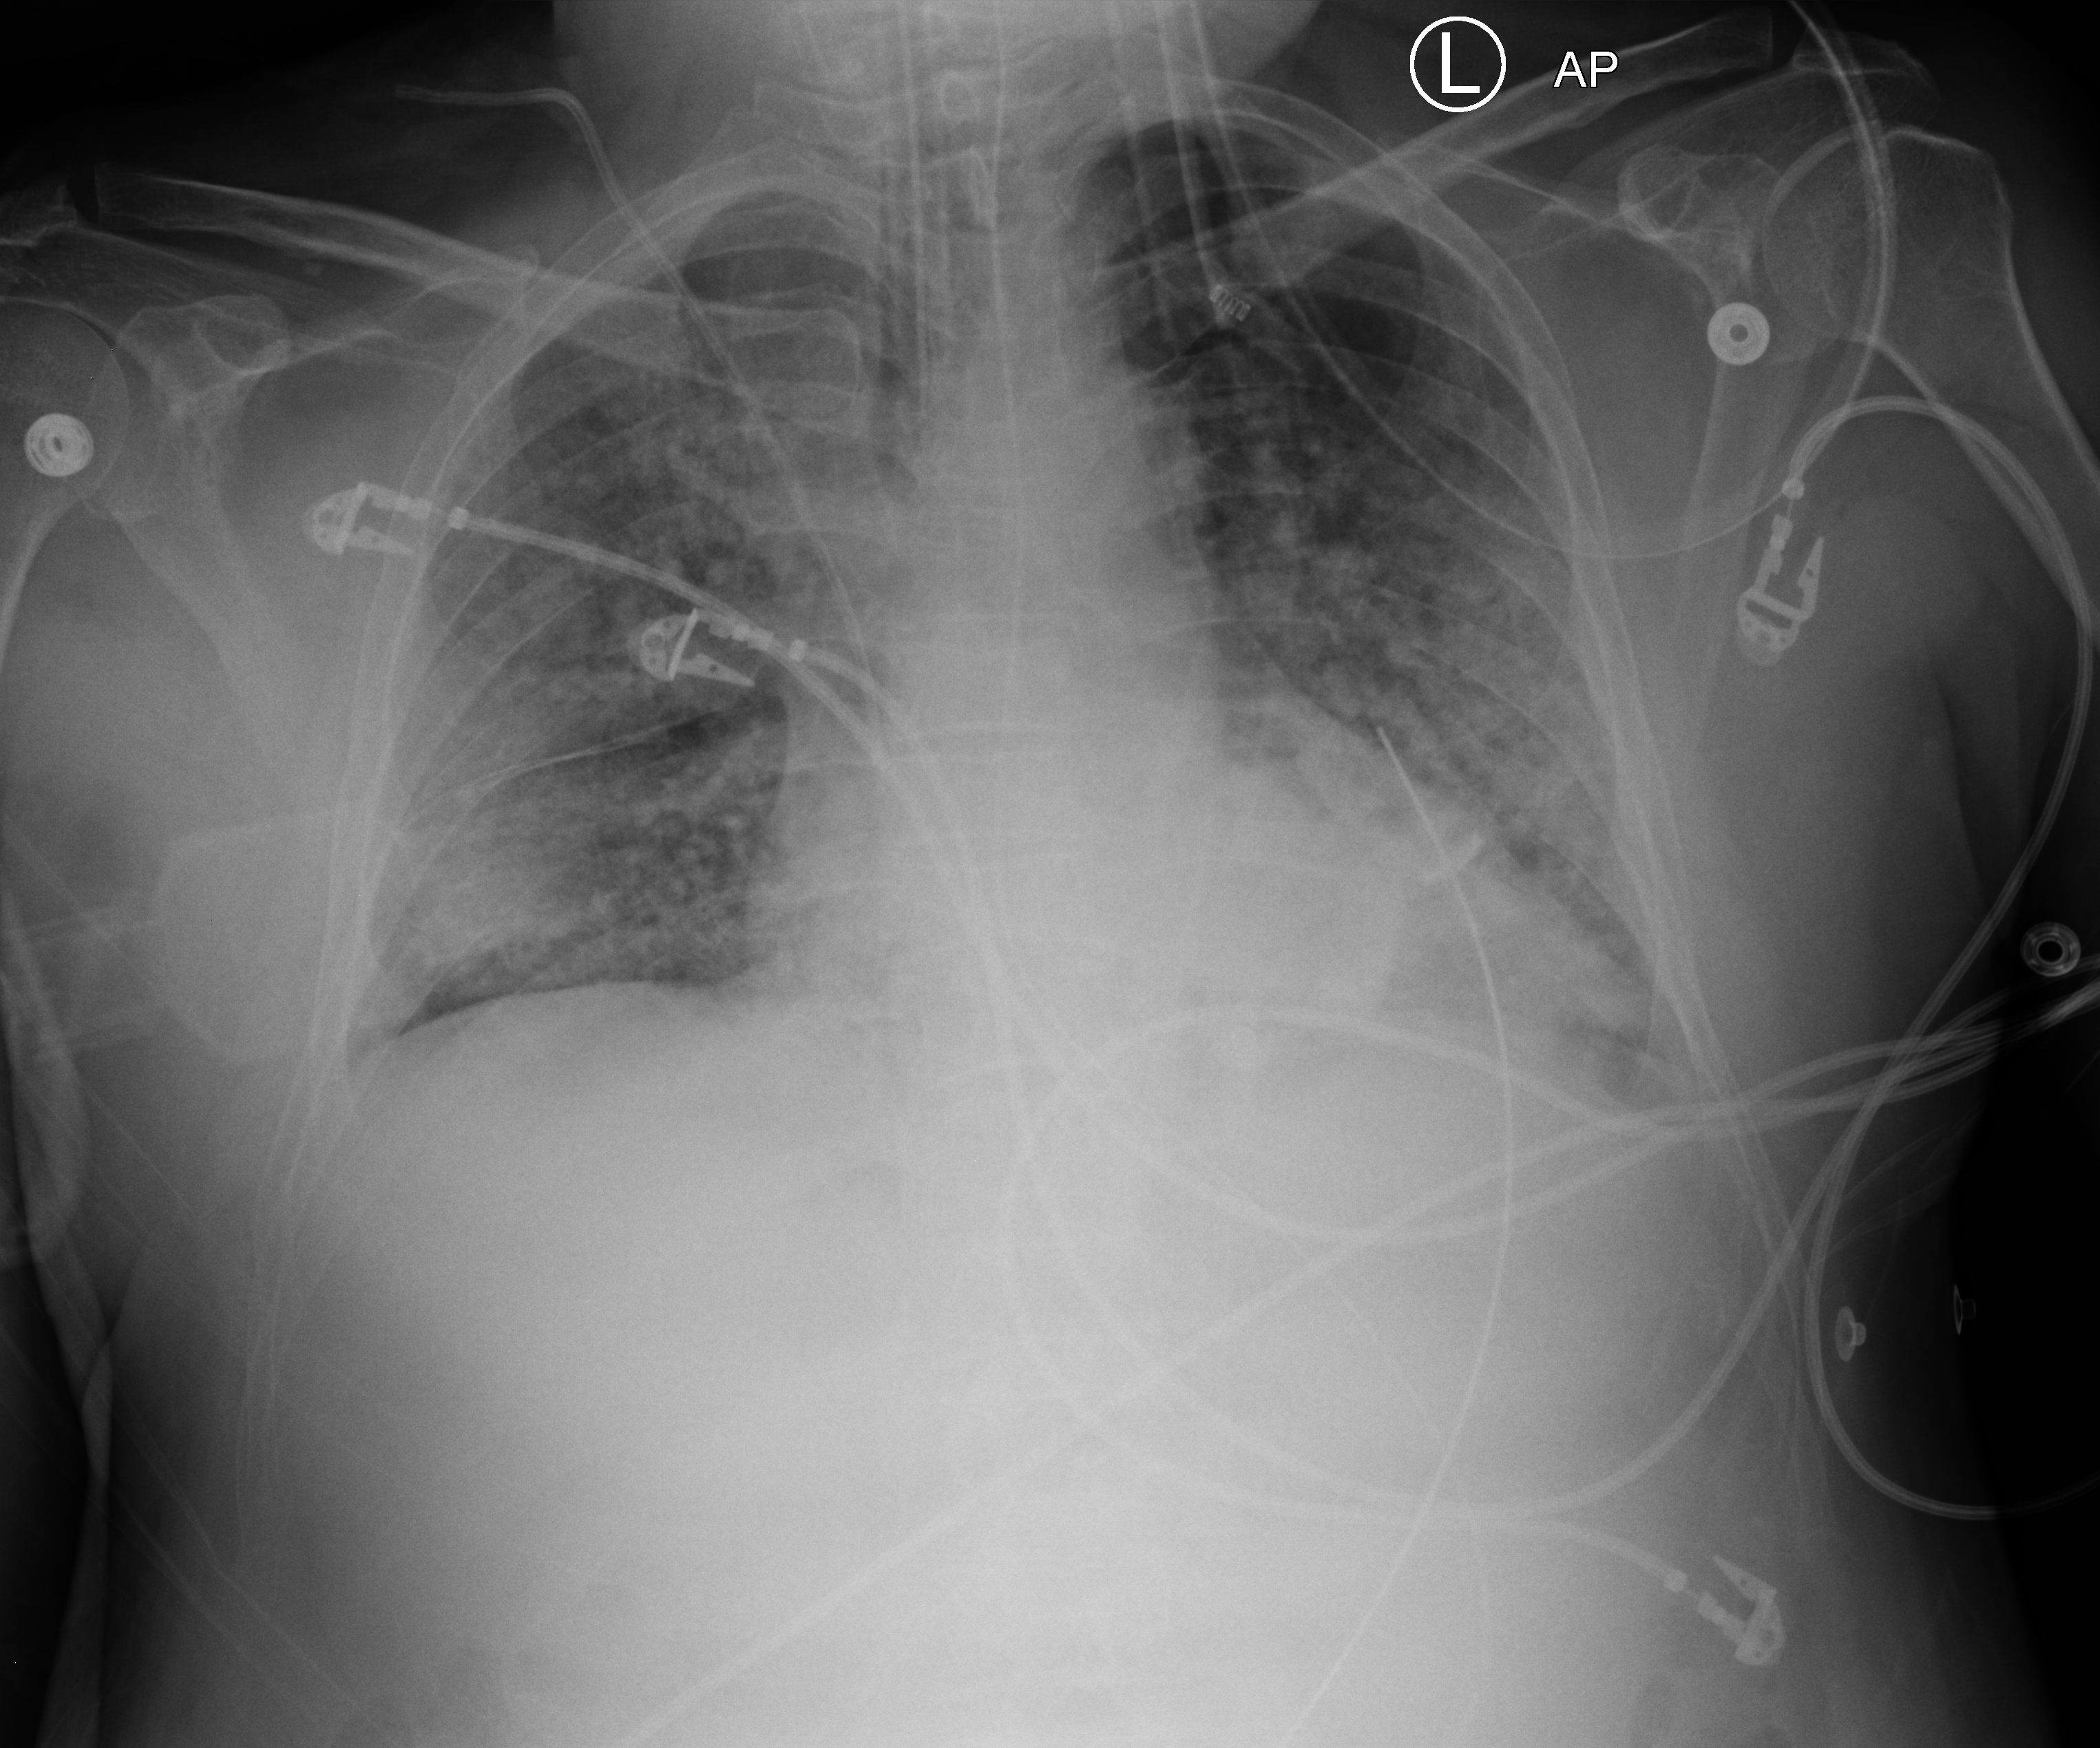
Portable chest radiograph, anteroposterior (AP) projection. Patient hospitalised with COVID-19; male, aged 60–74 years.
Hospital-stay facts (about this admission, not read from this image; timing relative to this image not recorded):
- length of hospital stay: 19 days